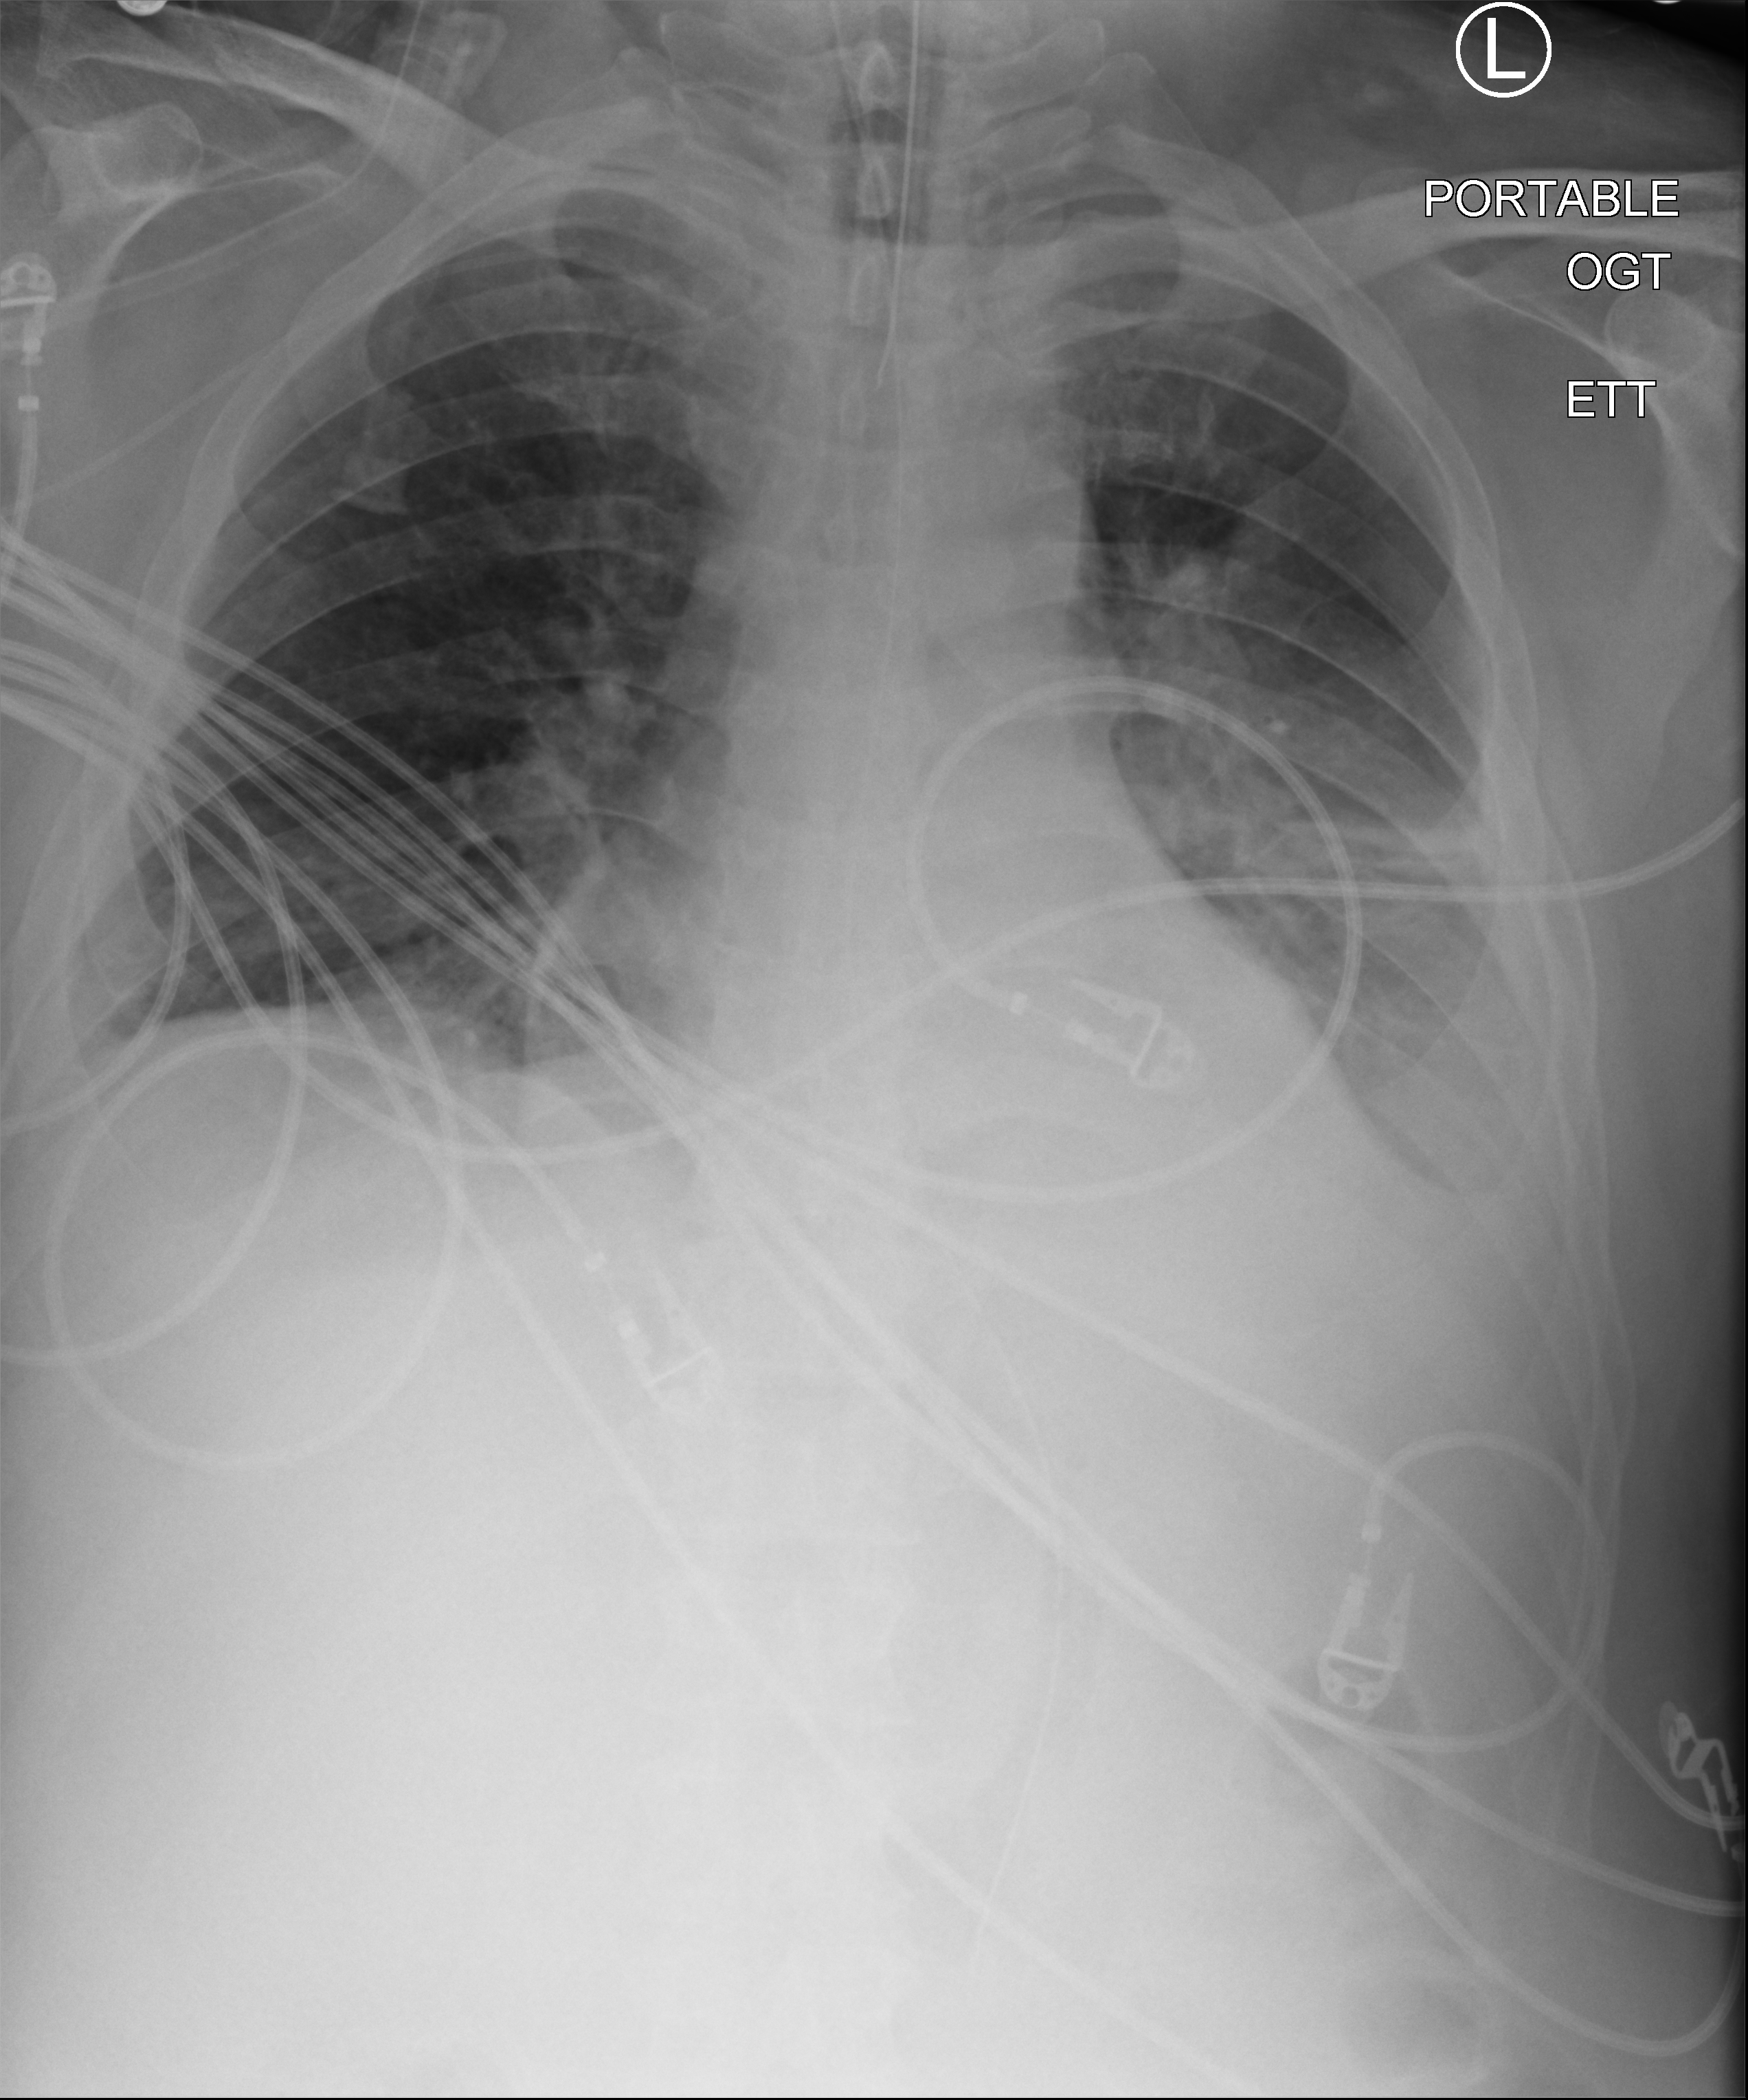
Chest X-ray (portable), anteroposterior (AP) projection. Patient hospitalised with COVID-19; male, aged 18–59 years.
Hospital-stay facts (about this admission, not read from this image; timing relative to this image not recorded): mechanically ventilated during this hospital stay: yes.